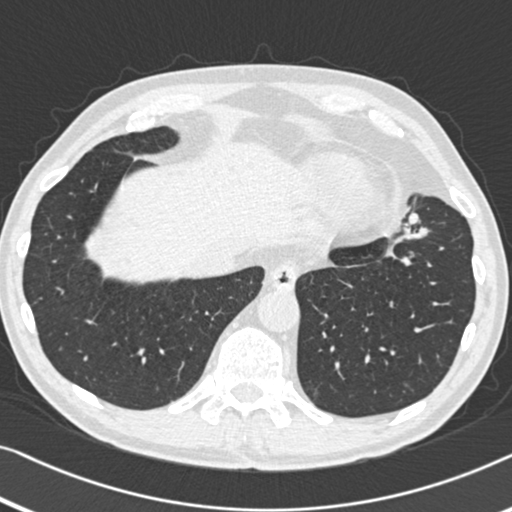
Low-dose screening chest CT, one axial slice; position 119 of 383 along the scan axis; reconstruction kernel B30f; lung window (W 1500 / L -600 HU); 512 × 512 image matrix.
Outlined on this slice (manually delineated by an expert):
- lesion 1 (tumor, upper lobe of left lung): bounding box (x1, y1, x2, y2) in pixels: (408, 213, 419, 225)